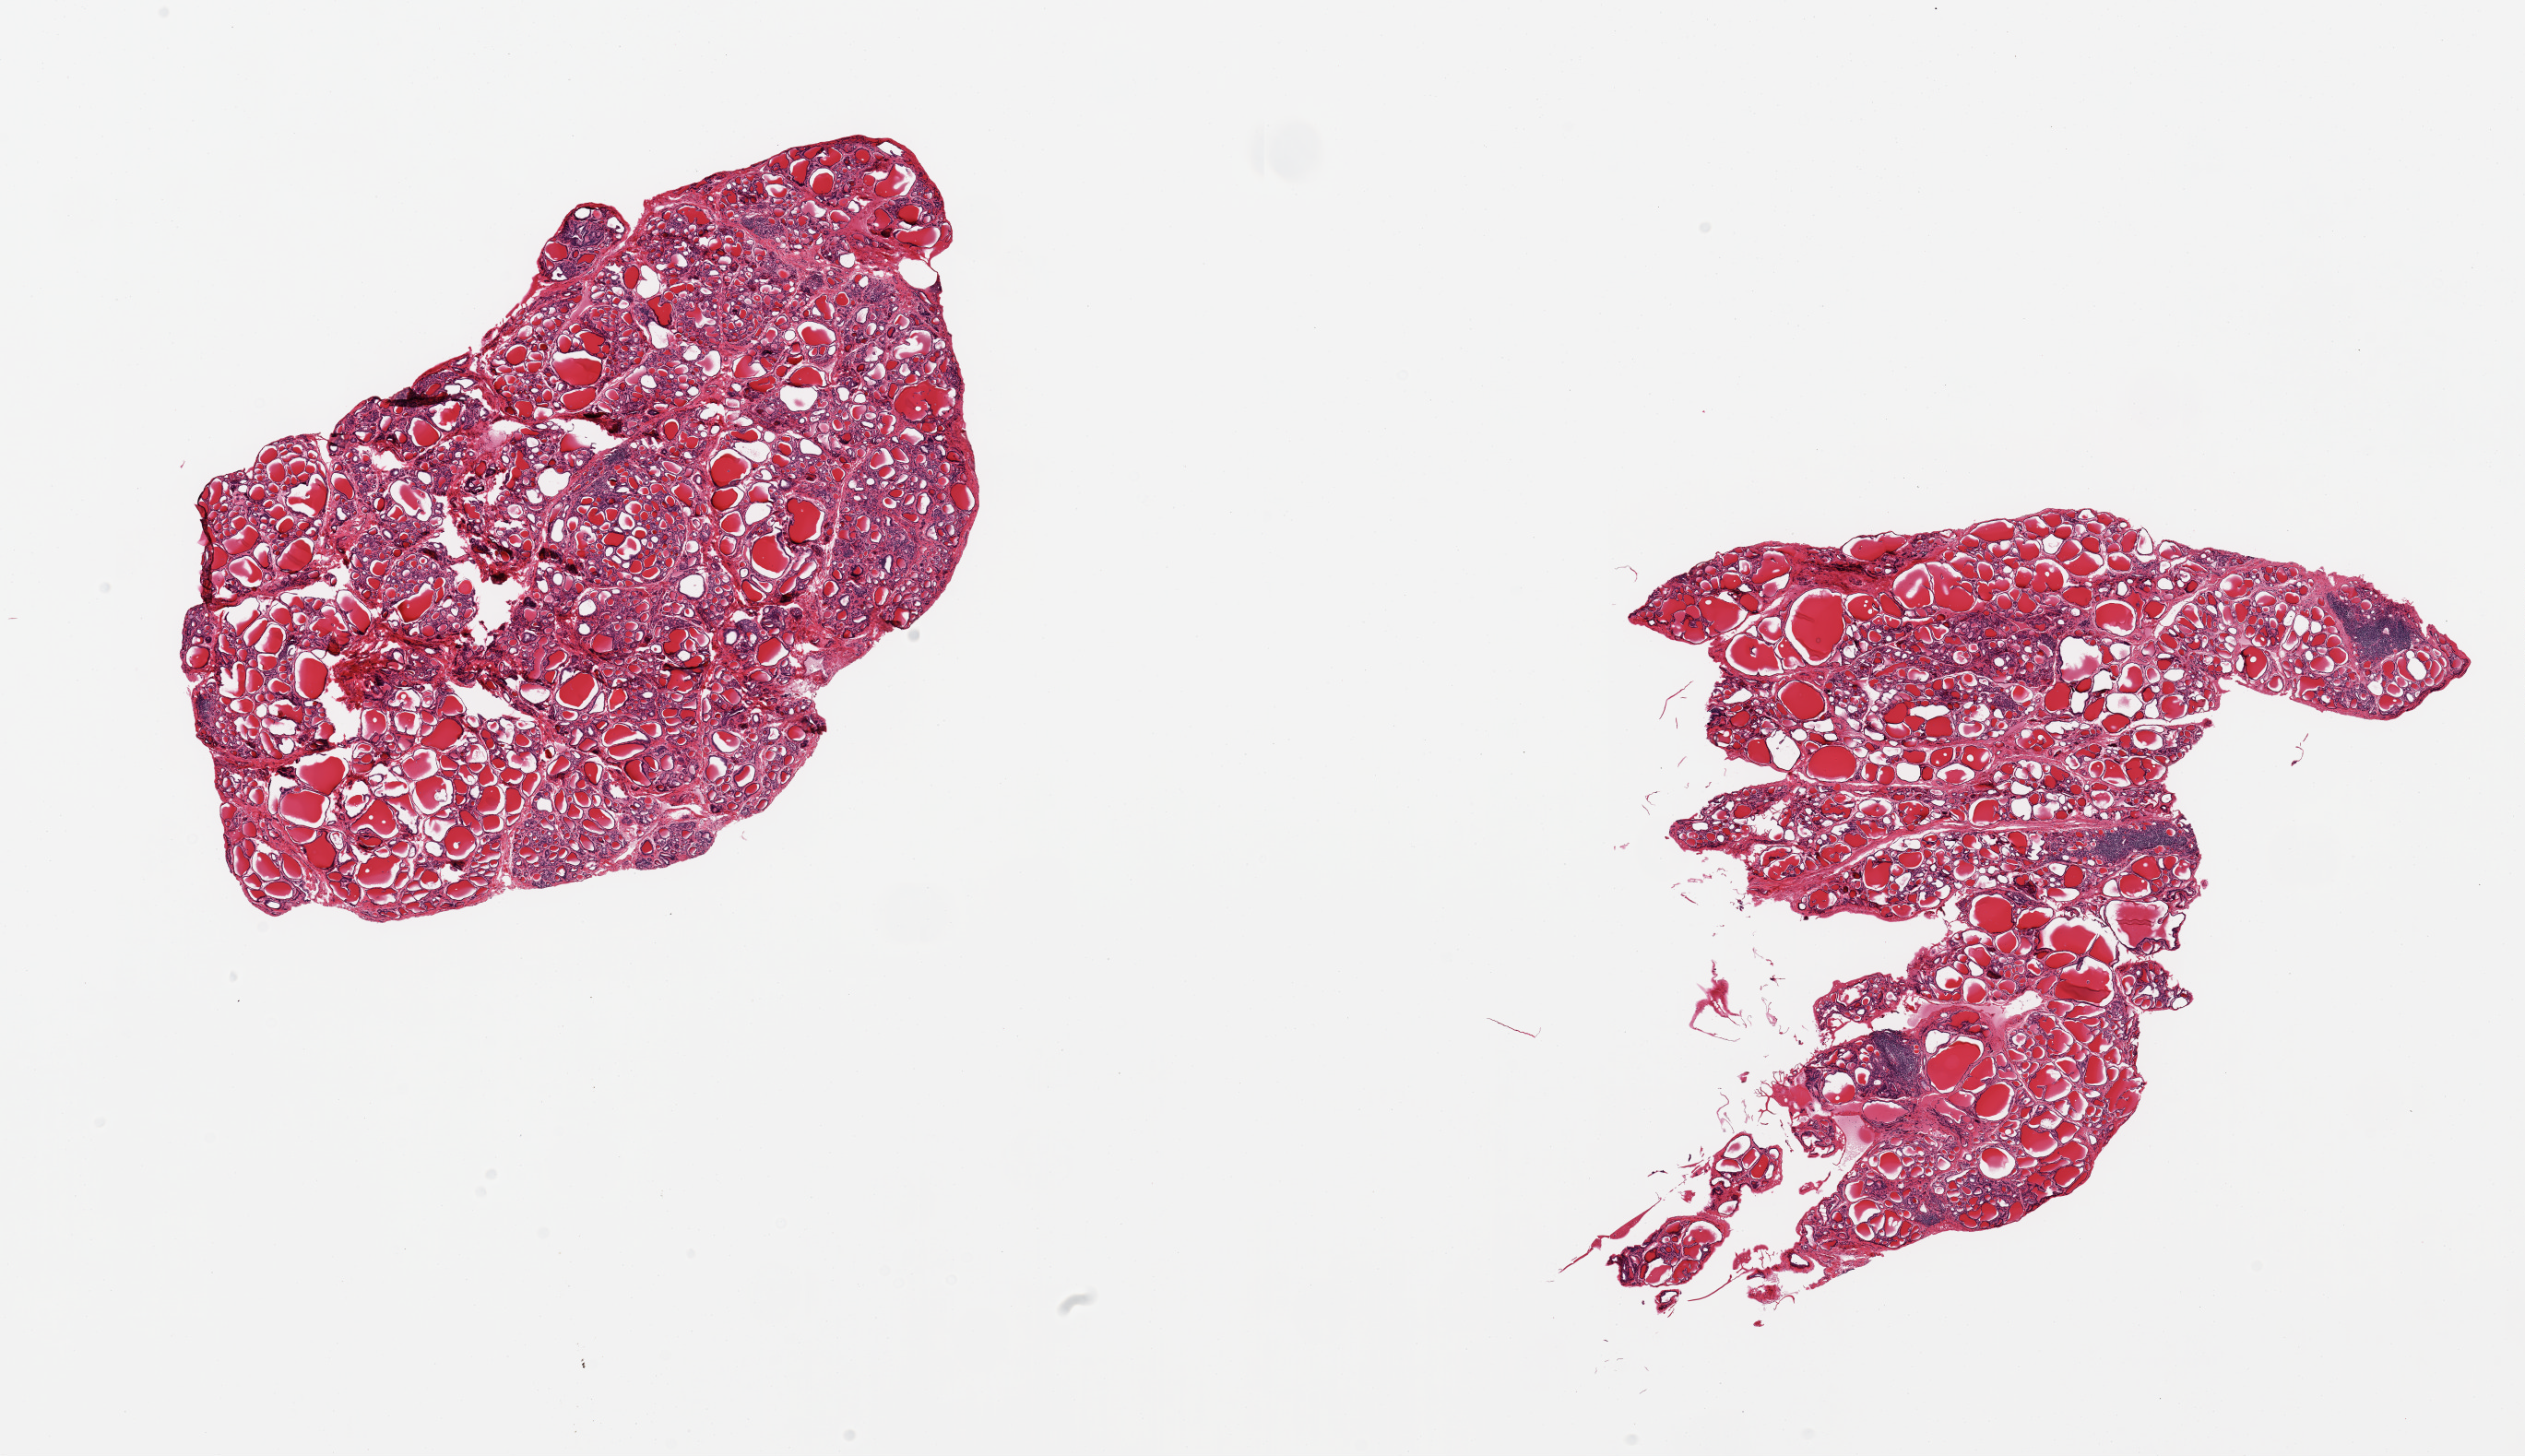
Digitized H&E-stained section — low-resolution overview of the scanned area, about 21.7 x 12.5 mm (from a 20x scan), PAXgene-fixed paraffin-embedded (PFPE) section, target tissue: thyroid, donor tissue sample. Donor: male.
Reviewer comment on this tissue sample: 2 pieces; scattered focal lymphocytic deposits, possible early Hashimoto thyroiditis.